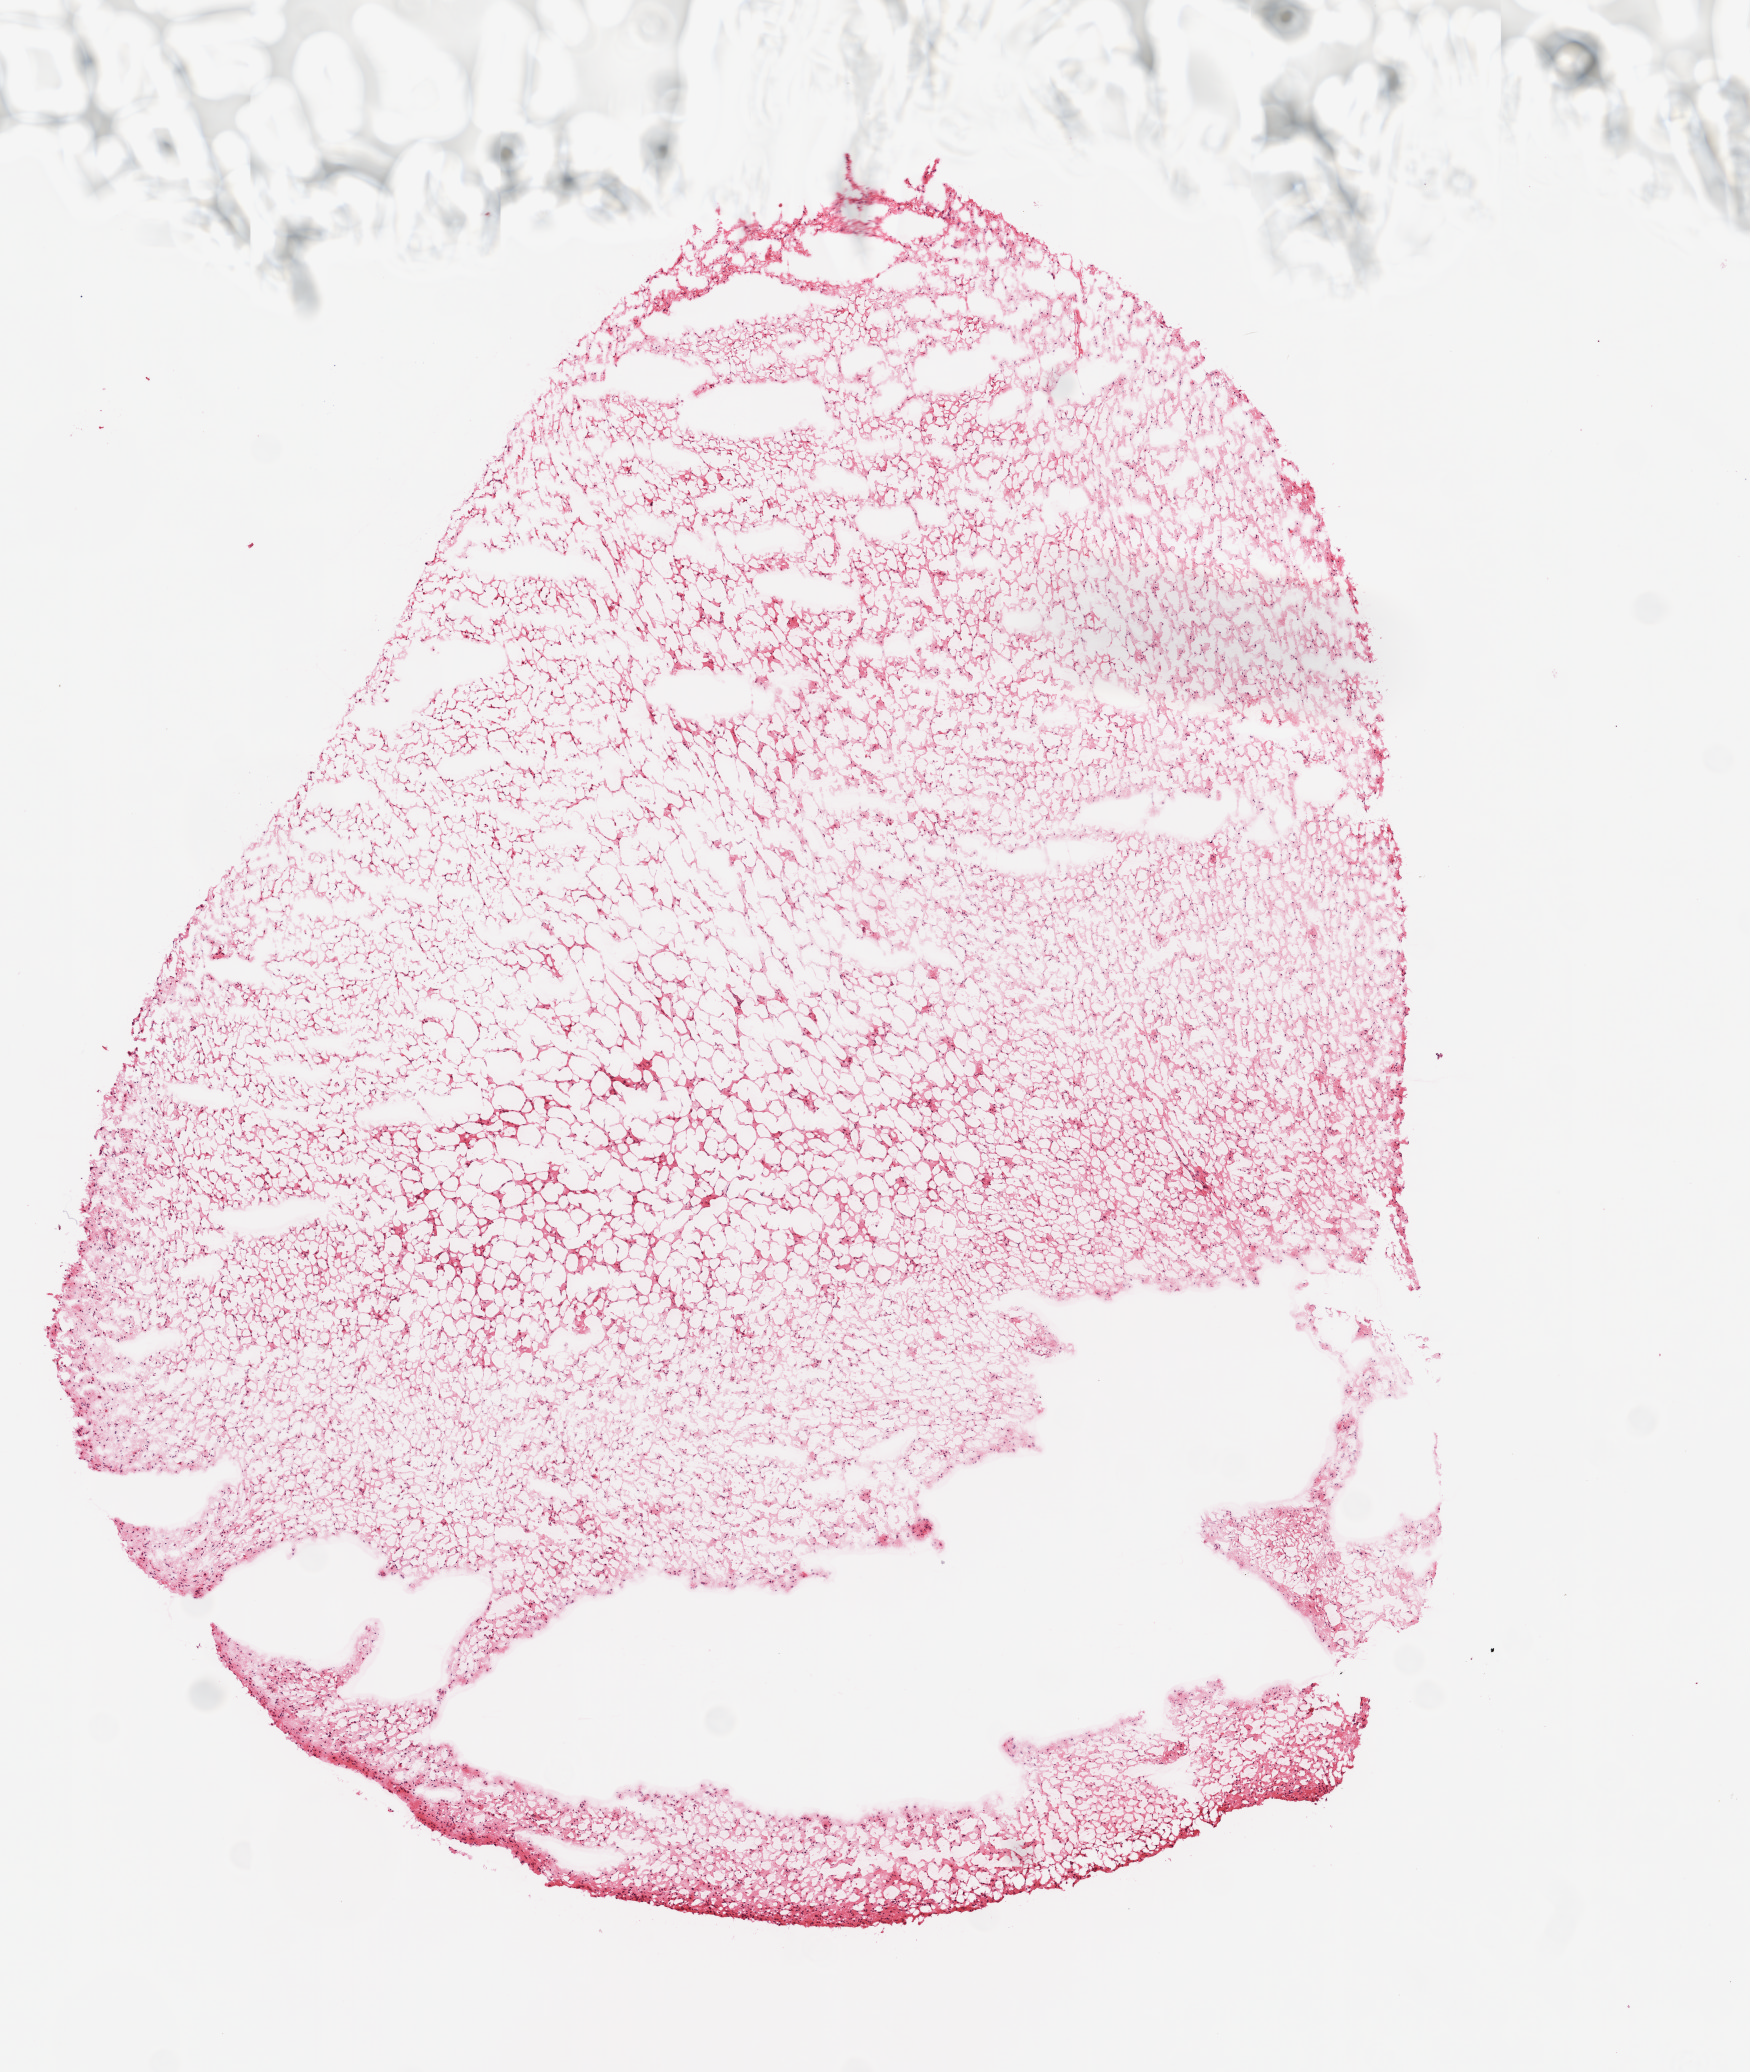
H&E whole-slide image, a low-resolution overview of the entire scanned area, about 7.0 x 8.3 mm (from a 20x scan); frozen section from the top of the tissue portion; primary tumour sample from the brain. Male, age 38 years at initial diagnosis. Histologic grade: G3 (poorly differentiated). Composition of this section per pathologist review: tumour cells 100%, tumour nuclei 65%, normal cells 0%, stromal cells 0%, necrosis 0%.
Diagnosis: Astrocytoma, anaplastic.